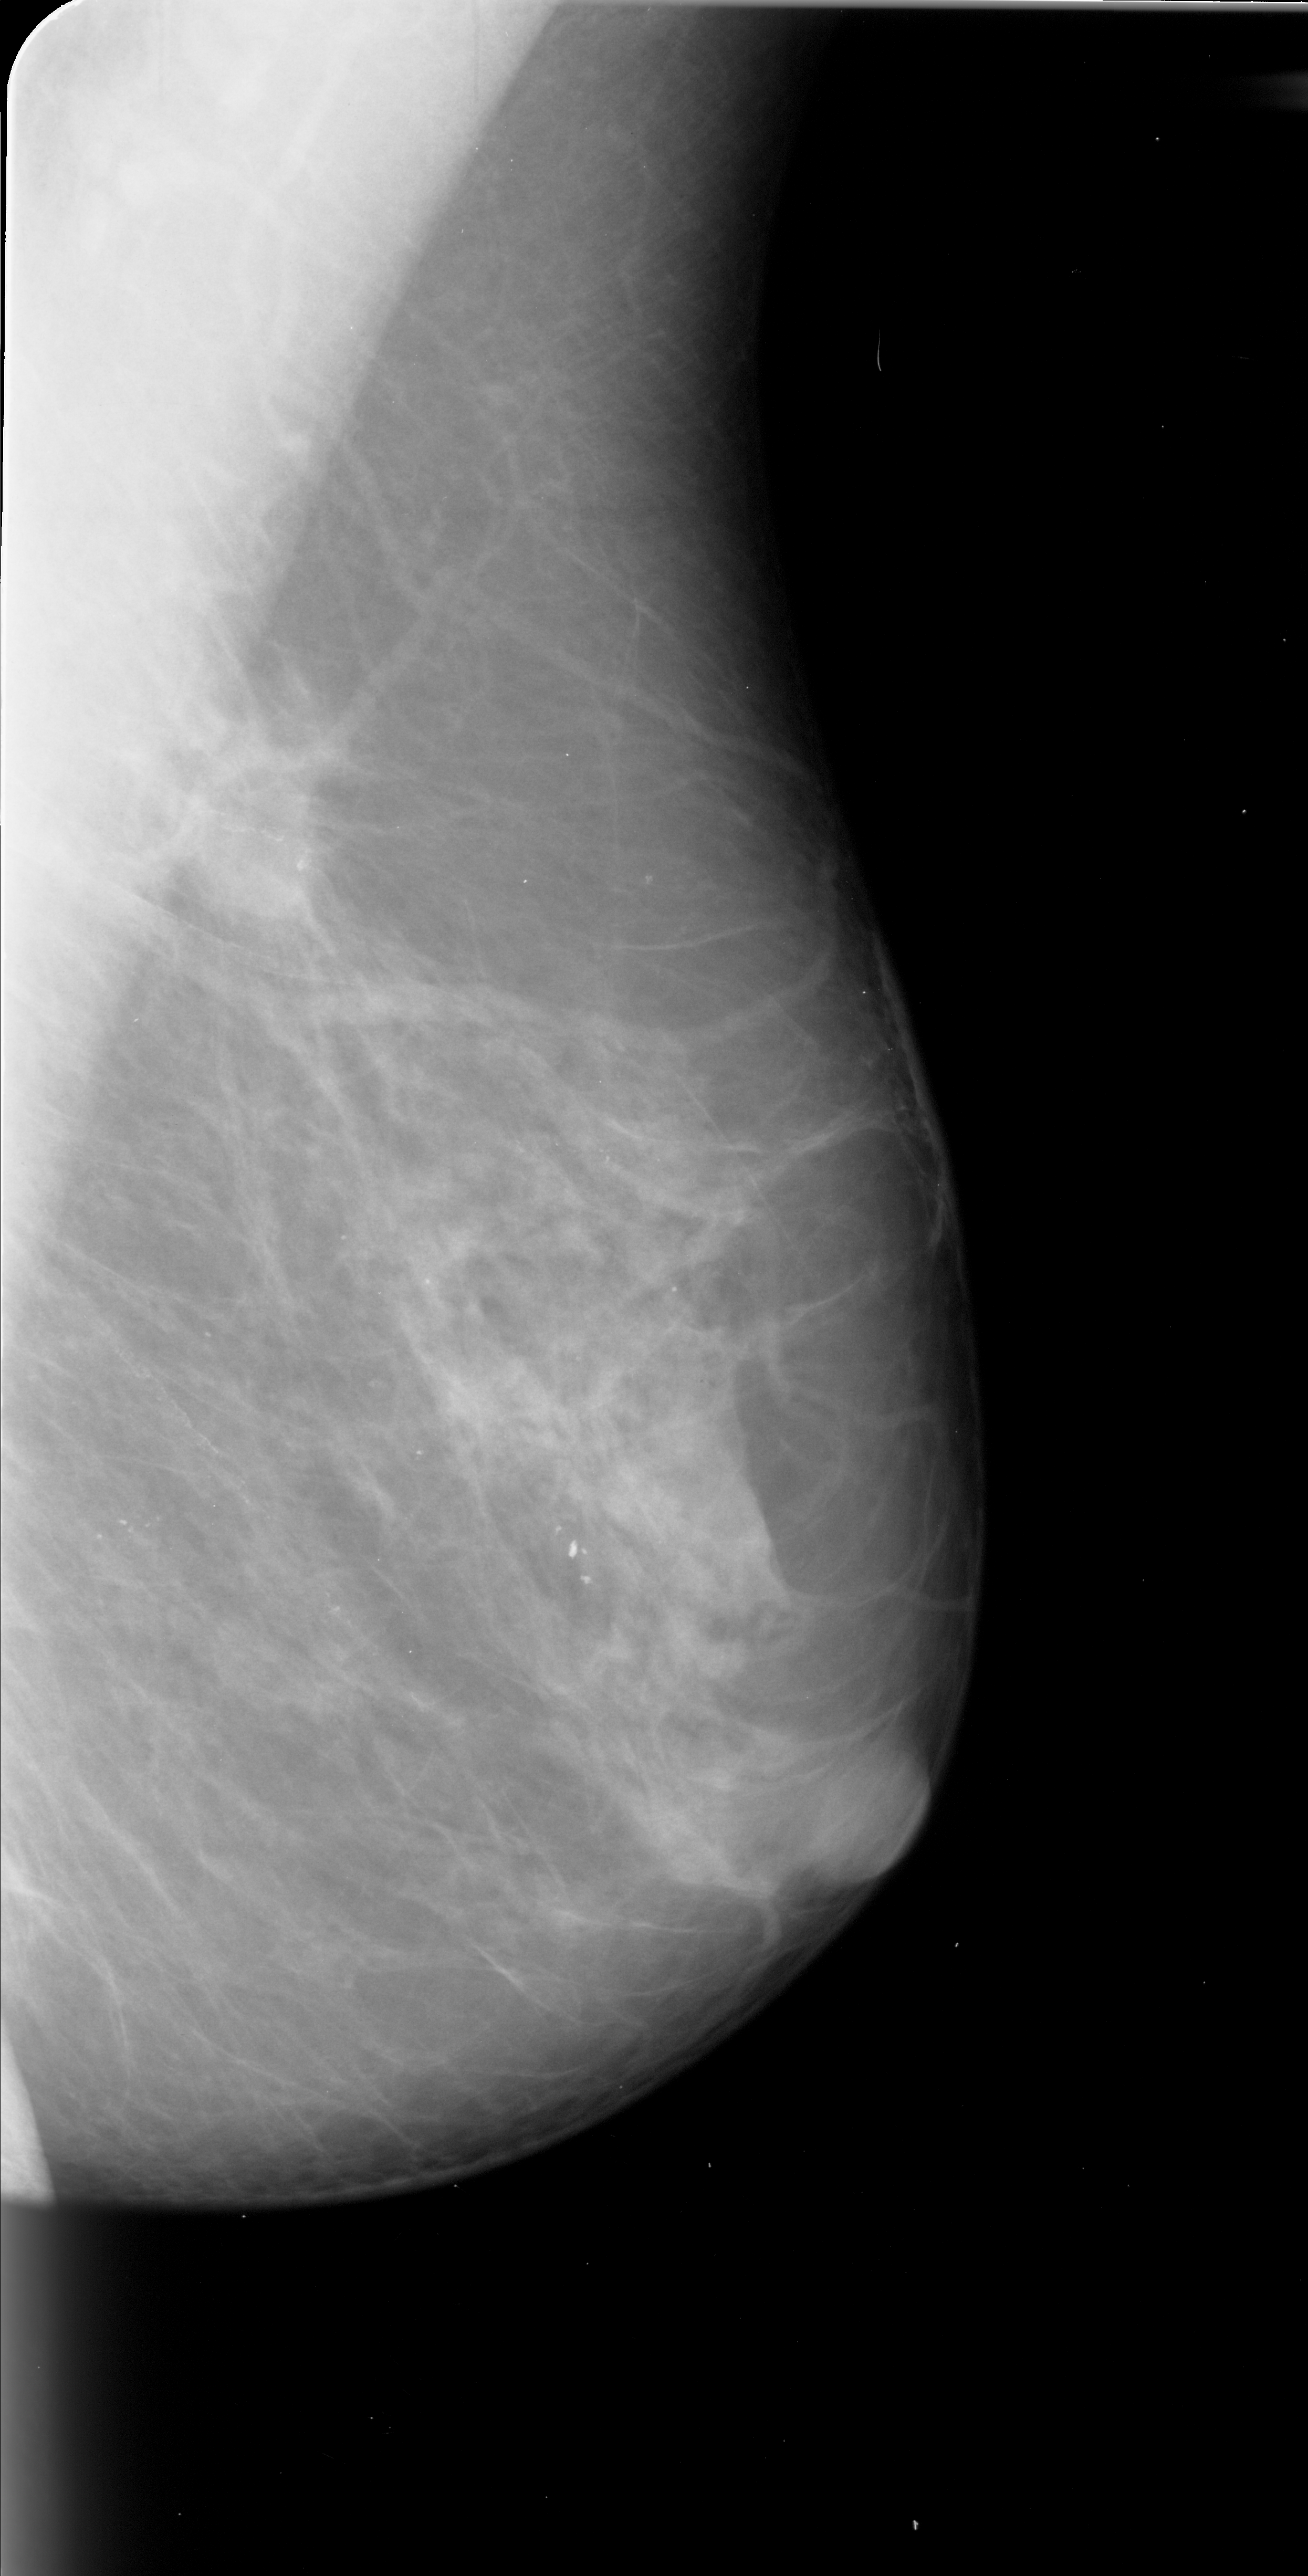
Scanned film-screen mammogram; right breast; mediolateral oblique (MLO) view; BI-RADS breast density category 2 (scale 1–4); 1308 × 2576 image matrix.
Expert-marked regions of interest on this film, with their recorded descriptors:
- mass, shape irregular, margins spiculated; BI-RADS assessment category 5; subtlety rating 4 on a 1 (subtle) to 5 (obvious) scale; pathology (as recorded): malignant: box from (x=139, y=727) to (x=348, y=942) px